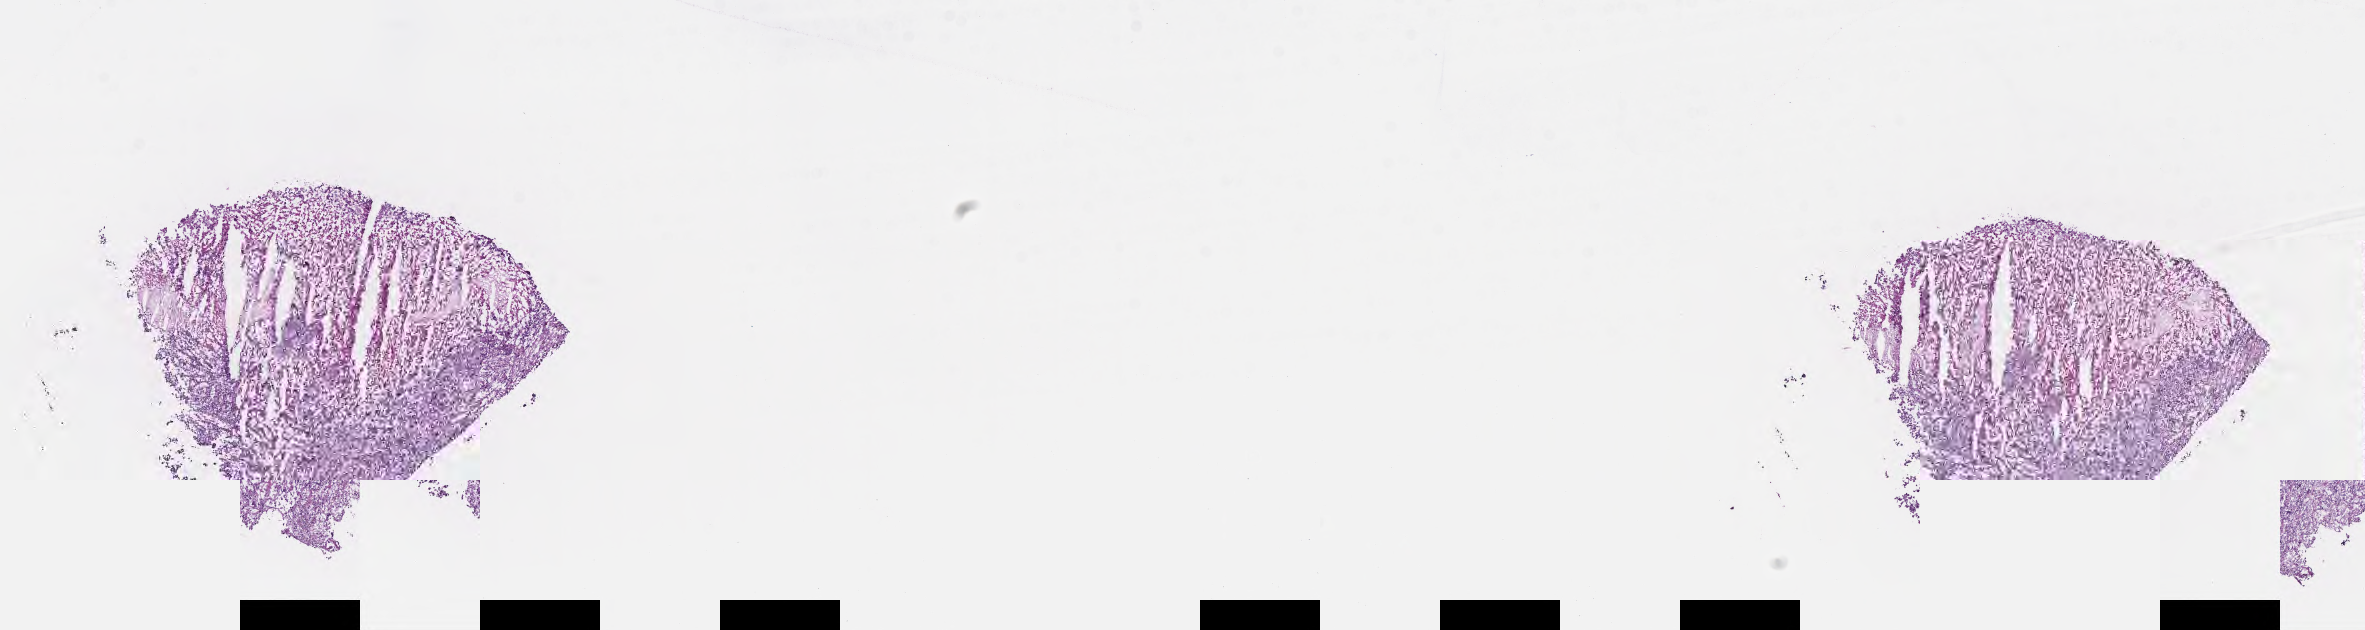
Whole-slide image, hematoxylin and eosin (H&E) stain — shown as a low-resolution overview of the whole scanned area (about 19.1 x 5.1 mm); cryosection; specimen: metastatic tumor tissue, resected from brain. Female, age 68 years at initial diagnosis. Pathologist review of this section (percent, as recorded): tumor cells 35%, tumor nuclei 35%, stromal cells 15%, necrosis 50%, normal cells 0%. Inflammatory infiltration, as recorded: lymphocyte infiltration 5%, monocyte infiltration 2%, neutrophil infiltration 4%.
Patient diagnosis (primary): Malignant melanoma, NOS.